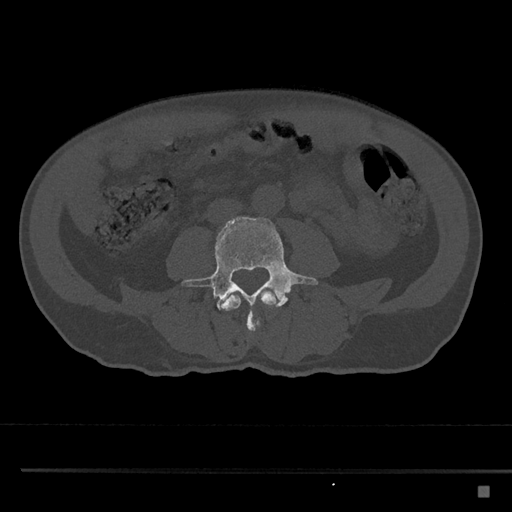
CT including the spine, one axial slice. Position 651 of 797 along the scan axis. Reconstruction kernel Br40s/3. 120 kVp. Bone window (W 1800 / L 400 HU). 0.5 mm slice thickness. 512 × 512 image matrix. Patient: male, 59 years. From the clinical record (not read from this slice): primary cancer: prostate.
Structures marked on this image (semi-automatically segmented with operator editing):
- L3 vertebra: bounding box <222,290,277,325> (left, top, right, bottom; pixels)
- L4 vertebra: <181,217,318,334>